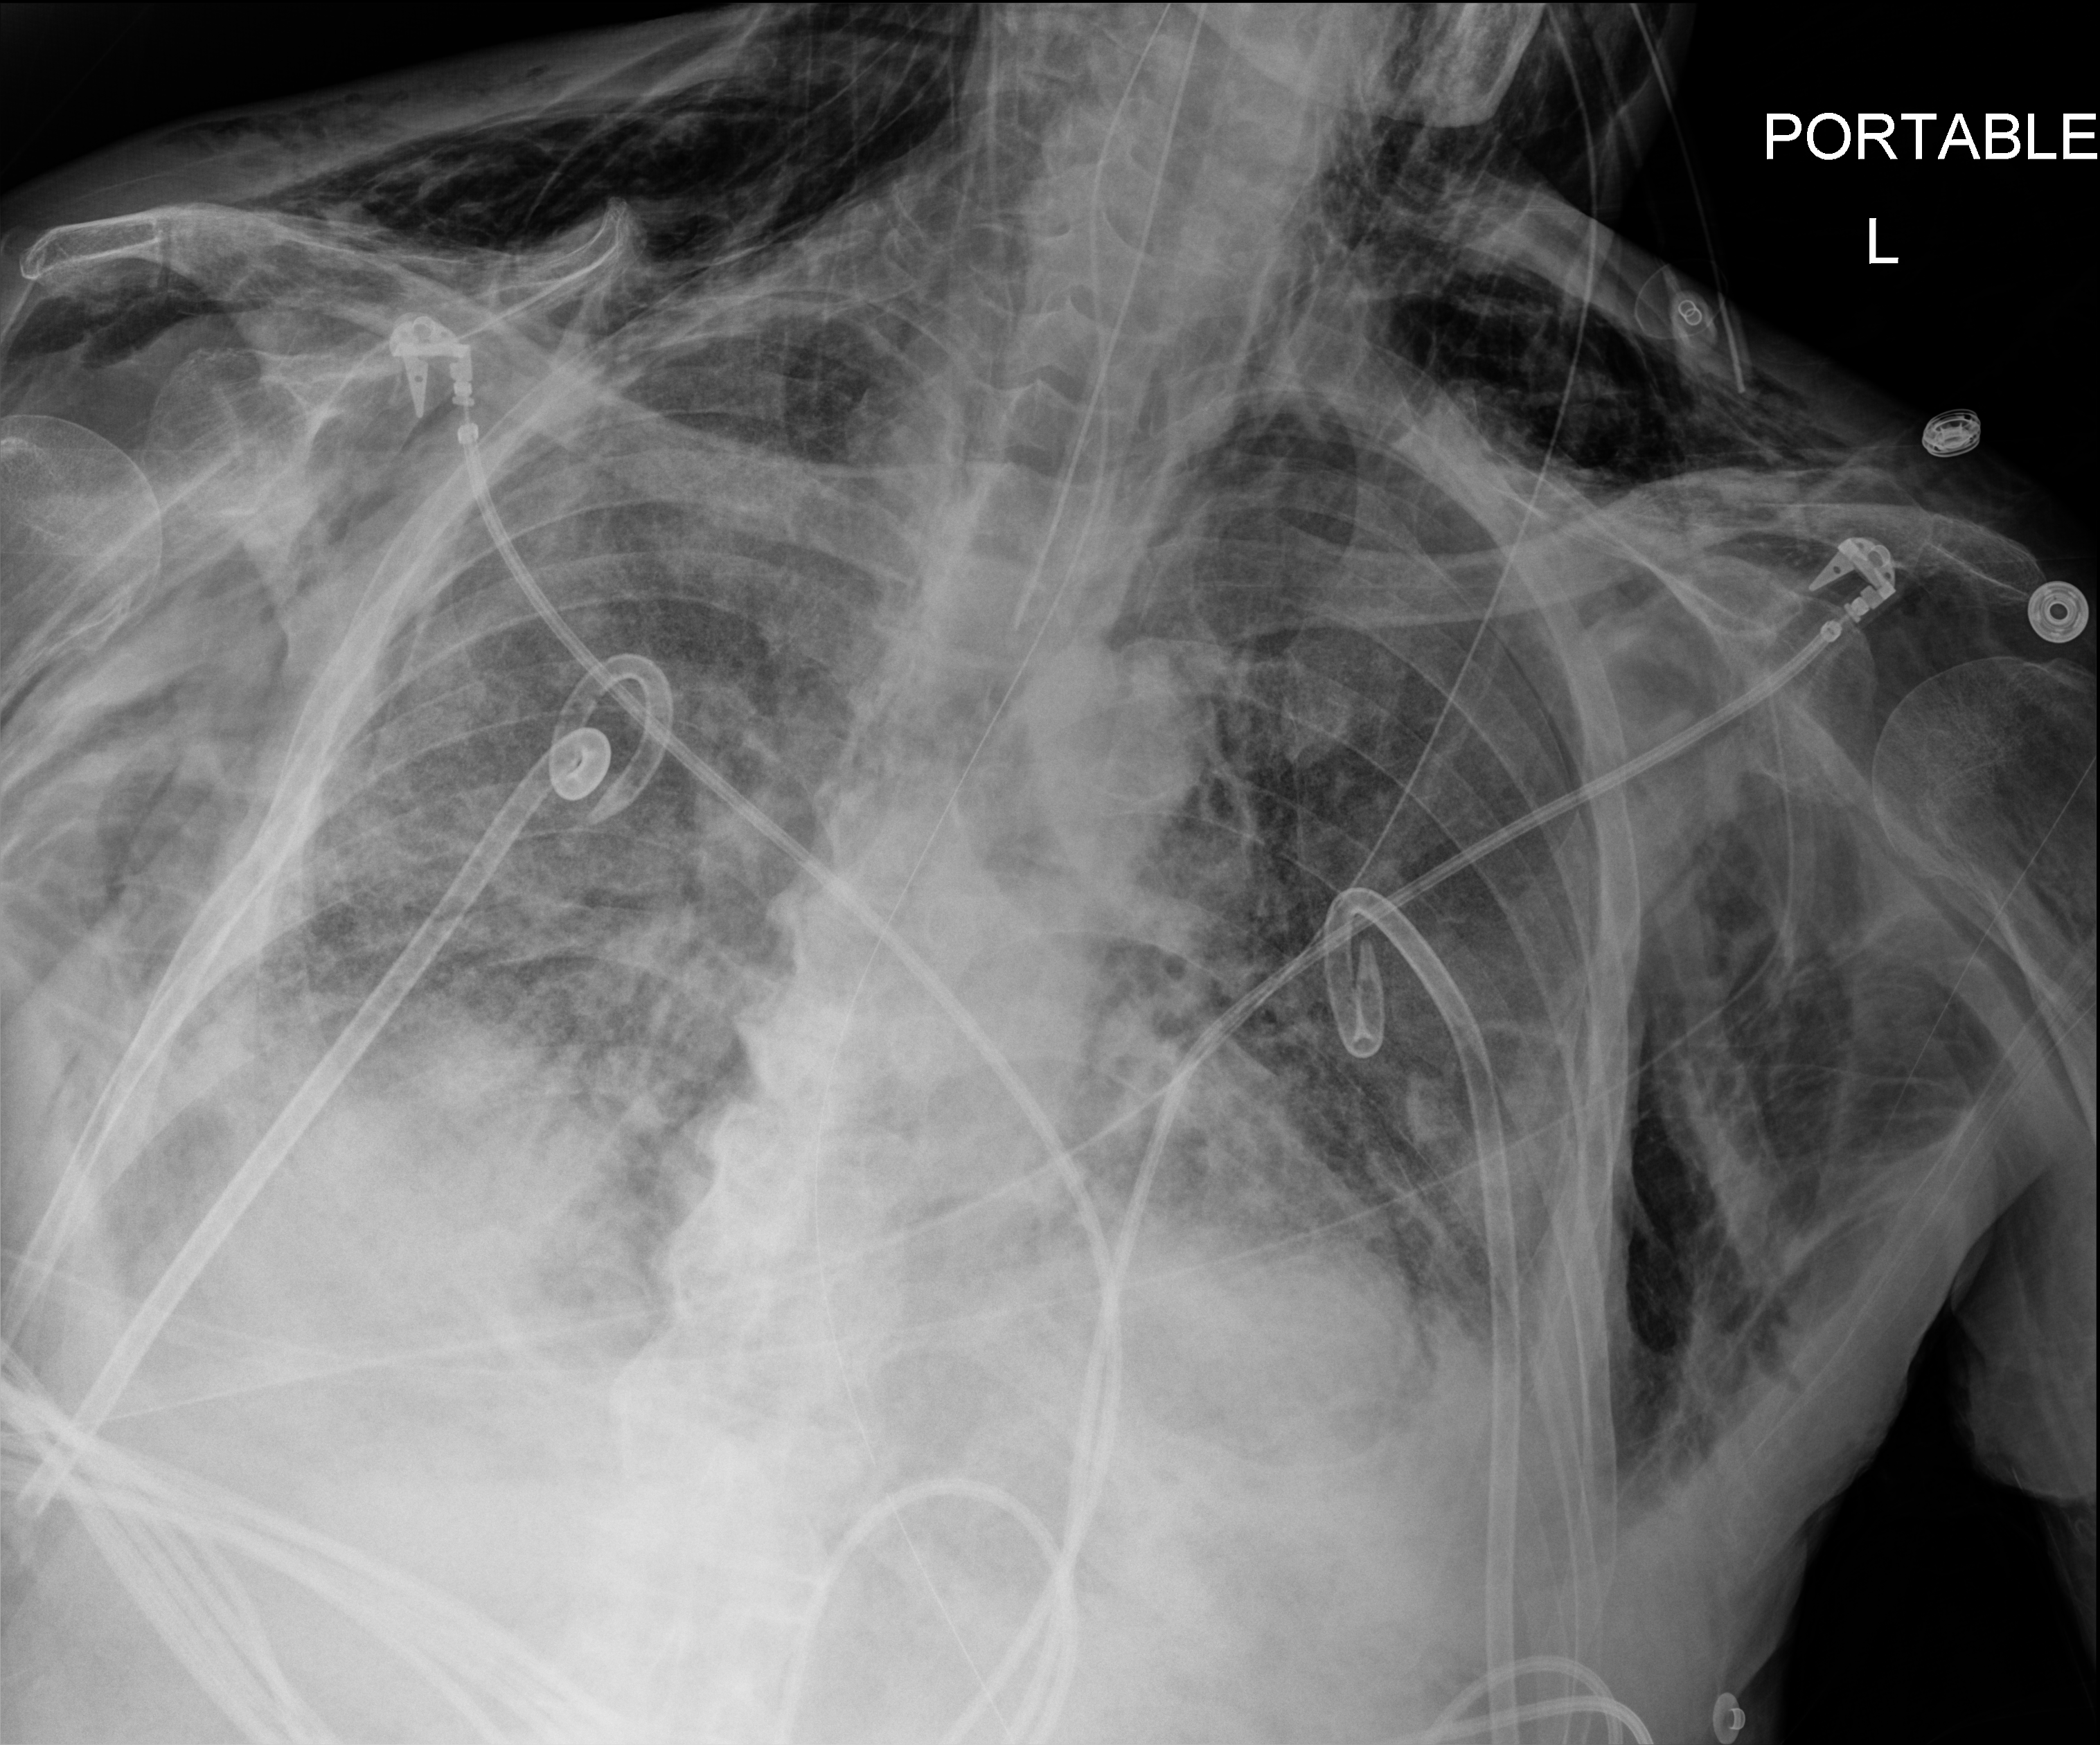
Bedside chest radiograph (digital radiography), anteroposterior (AP) projection. Male patient hospitalised with COVID-19, age 75–90 years.
Hospital-stay facts (about this admission, not read from this image; timing relative to this image not recorded):
- admitted to intensive care during this hospital stay: yes
- hypertension (admission record): yes